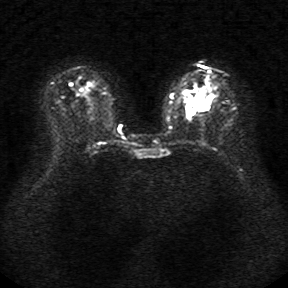
Breast MRI, one axial slice. Diffusion-weighted series; image 2 of 4 stored at this slice position (different b-values; order by instance number). 1.5 T. 288 × 288 image matrix, field of view 340 × 340 mm. Female patient.
Outlined on this slice (expert manual segmentation):
- tumour on diffusion-weighted imaging: box from (x=194, y=96) to (x=206, y=110) px